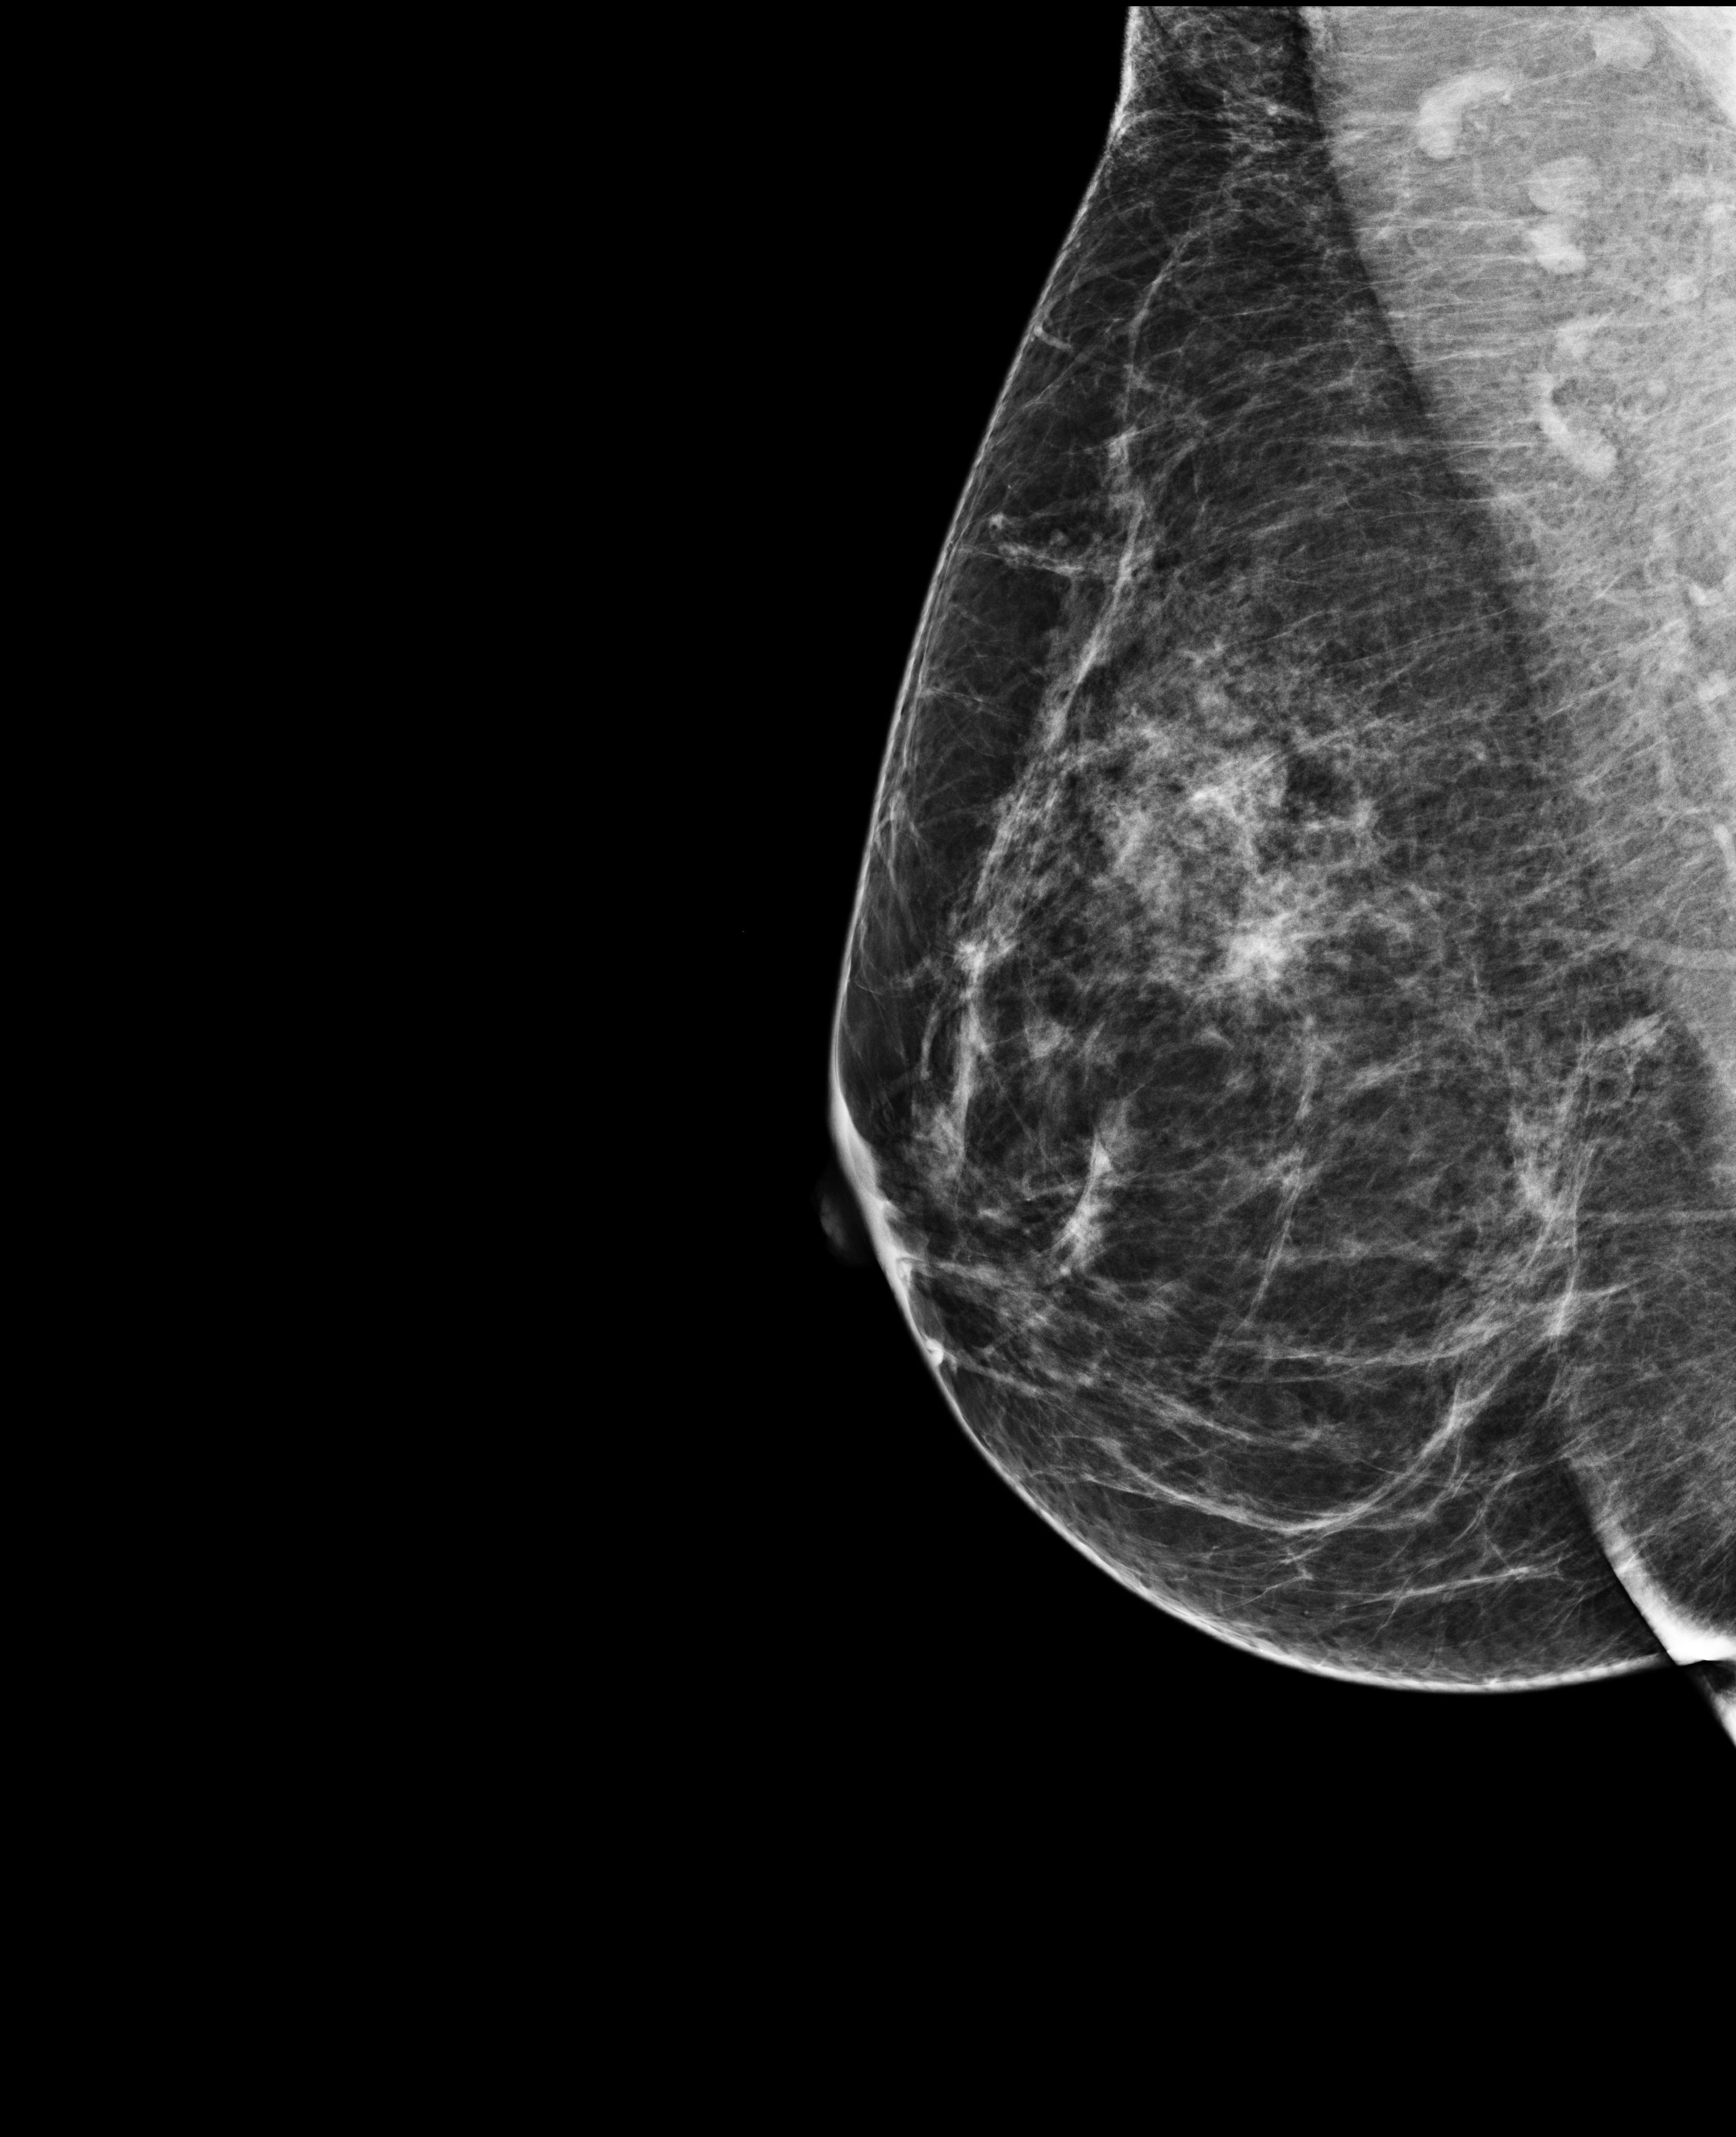
Screening examination; compressed breast thickness 64 mm. Patient aged 52 years (female).
Image type: full-field digital mammogram. Breast: right. Projection: medio-lateral oblique projection.